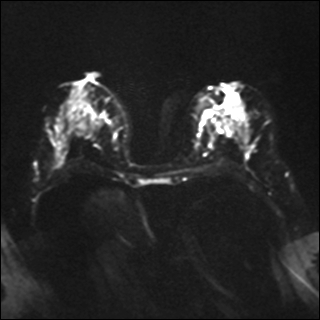
Breast MRI, one axial slice; slice 17 of 35 in the series (ordered by position); diffusion-weighted series; image 2 of 4 stored at this slice position (different b-values; order by instance number); 1.5 T; 320 × 320 image matrix. Female patient.
Annotated regions visible in this slice (outlined manually by an expert reader):
- tumour on diffusion-weighted imaging: bounding box (x1, y1, x2, y2) in pixels: (212, 103, 233, 128)